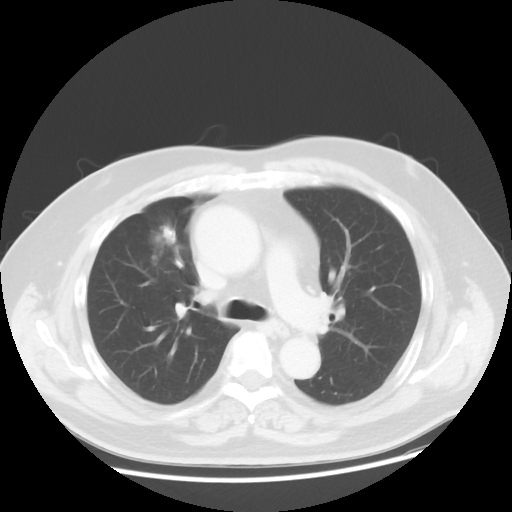
Chest CT, one axial slice. Reconstruction kernel STANDARD. 120 kVp. Lung window (W 1500 / L -600 HU). 5 mm slice thickness. 512 × 512 image matrix, field of view 392 × 392 mm. Male patient, age 60 years. From the clinical record (not read from this slice): clinical TNM (as recorded): T2 N3 M0; histopathological grade: G2-3.
Structures marked on this image (rectangle marked by the reading radiologist):
- lung tumour (recorded histology: adenocarcinoma): box from (x=145, y=213) to (x=187, y=257) px